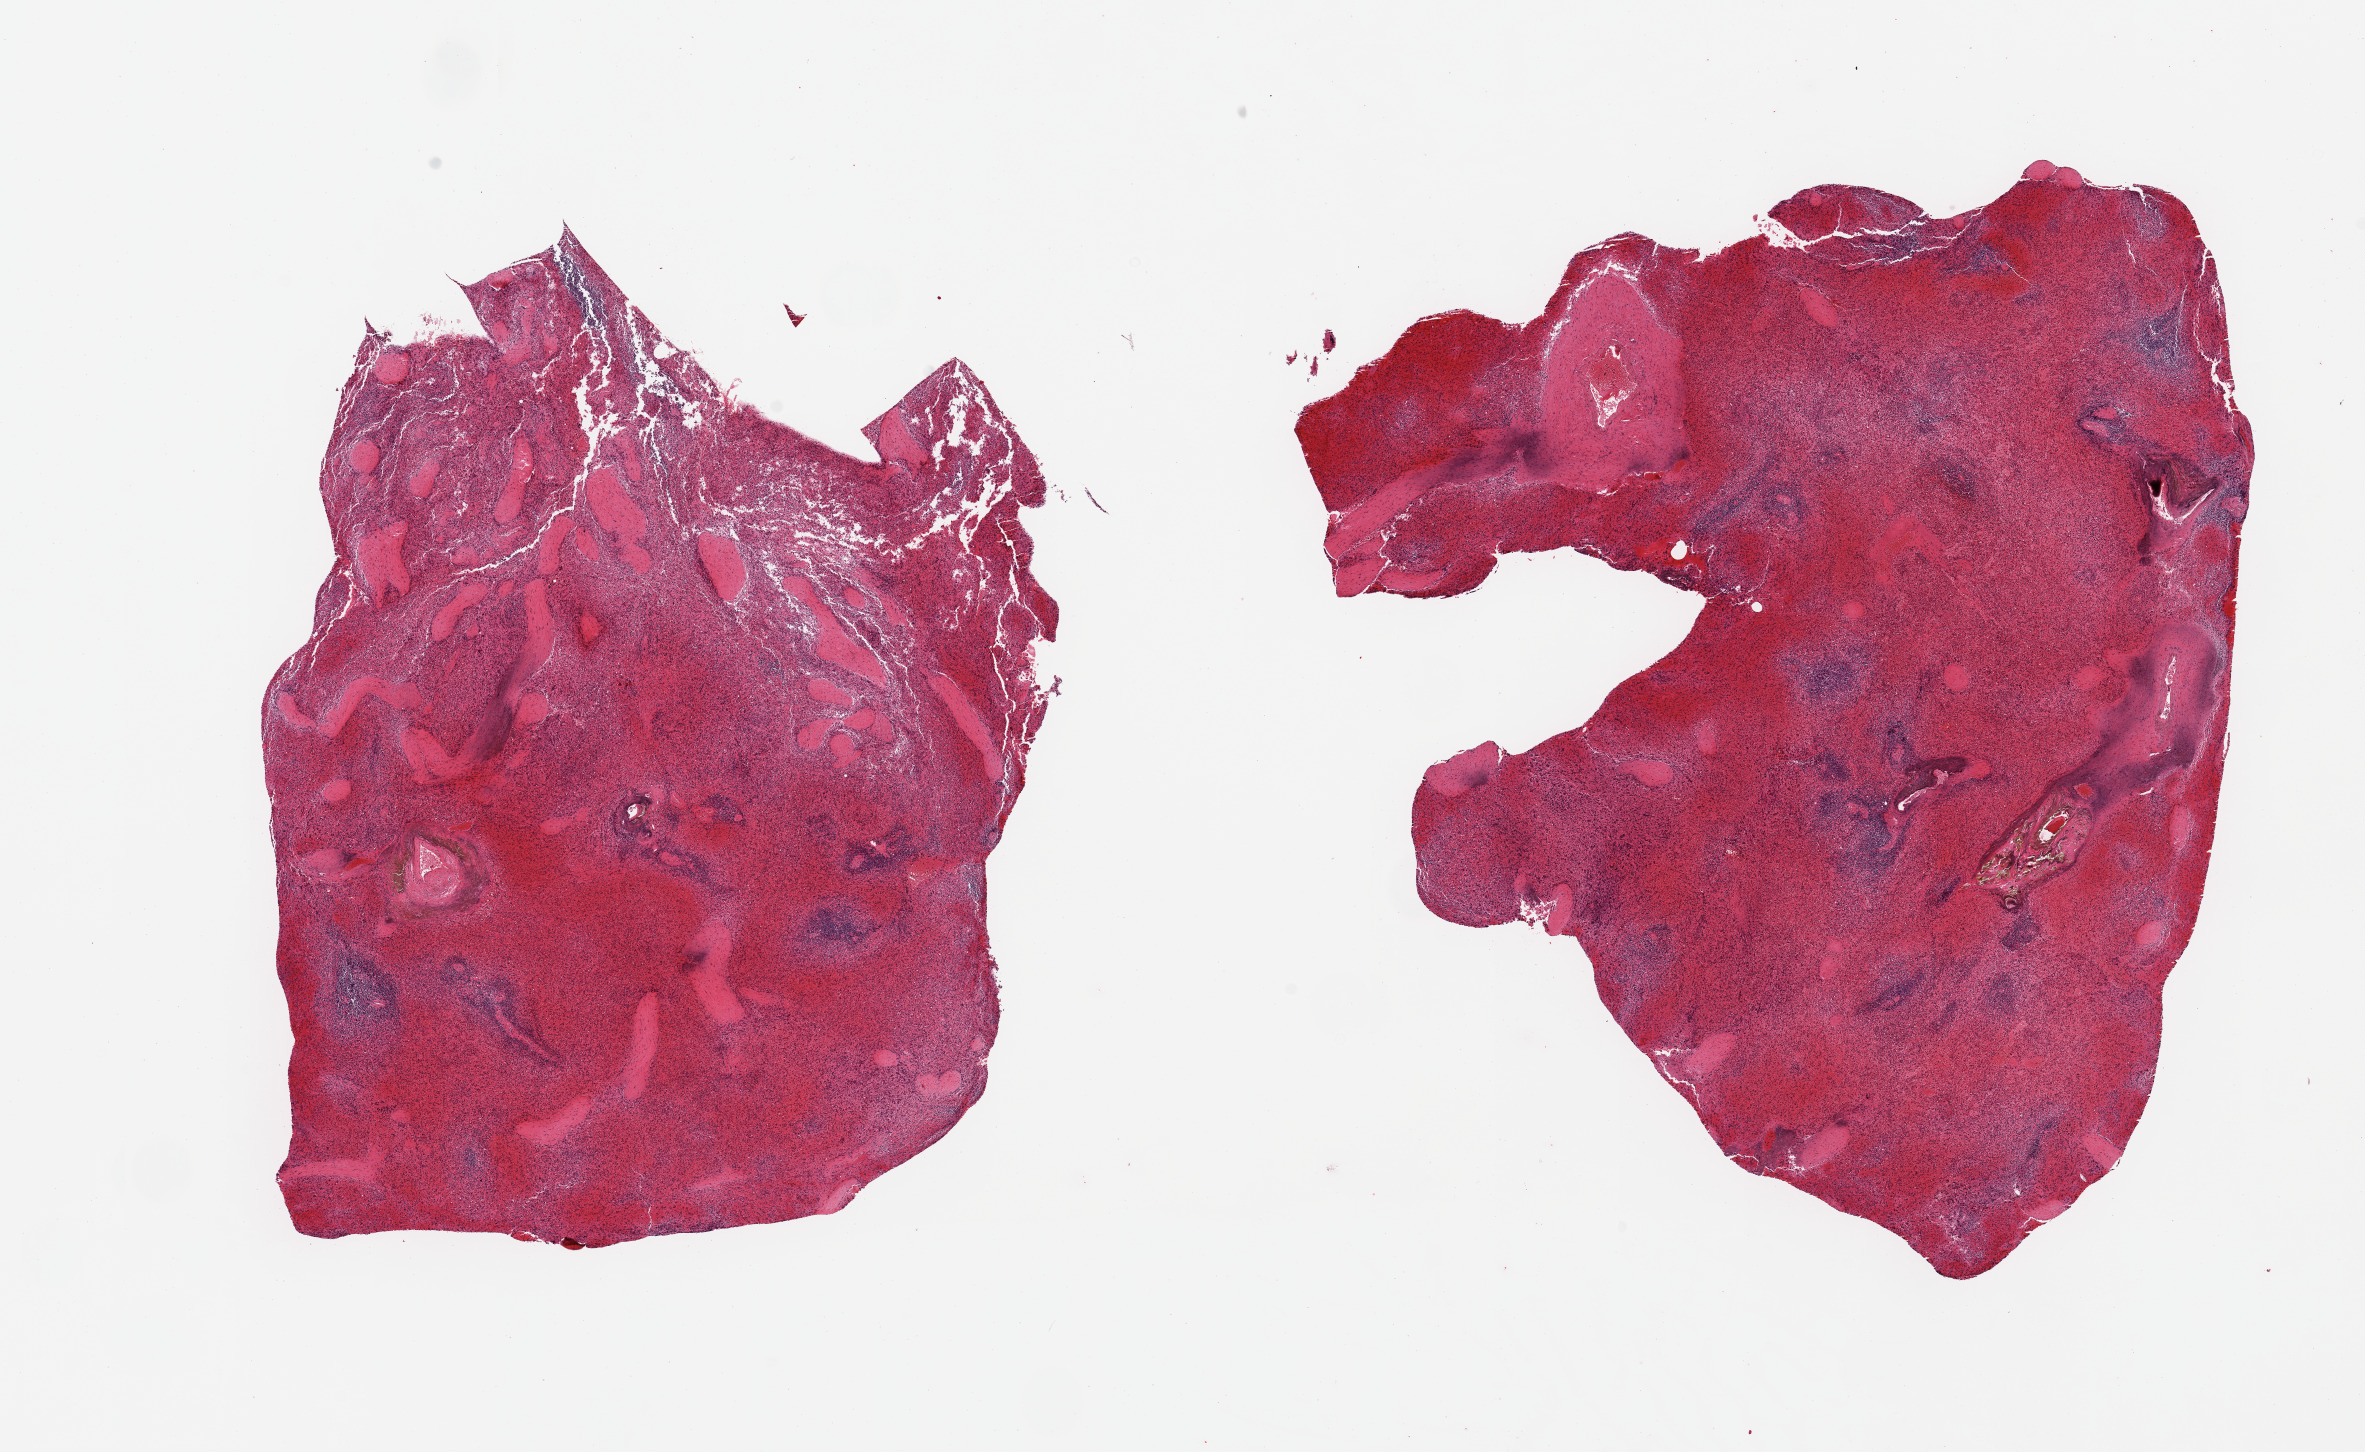
Digitized H&E-stained section — a low-resolution overview of the entire scanned area, about 18.7 x 11.5 mm; PAXgene-fixed paraffin-embedded (PFPE) section; section of spleen (target tissue); donor tissue sample. Donor: male.
* review note (as recorded): 2 pieces, marked congestion